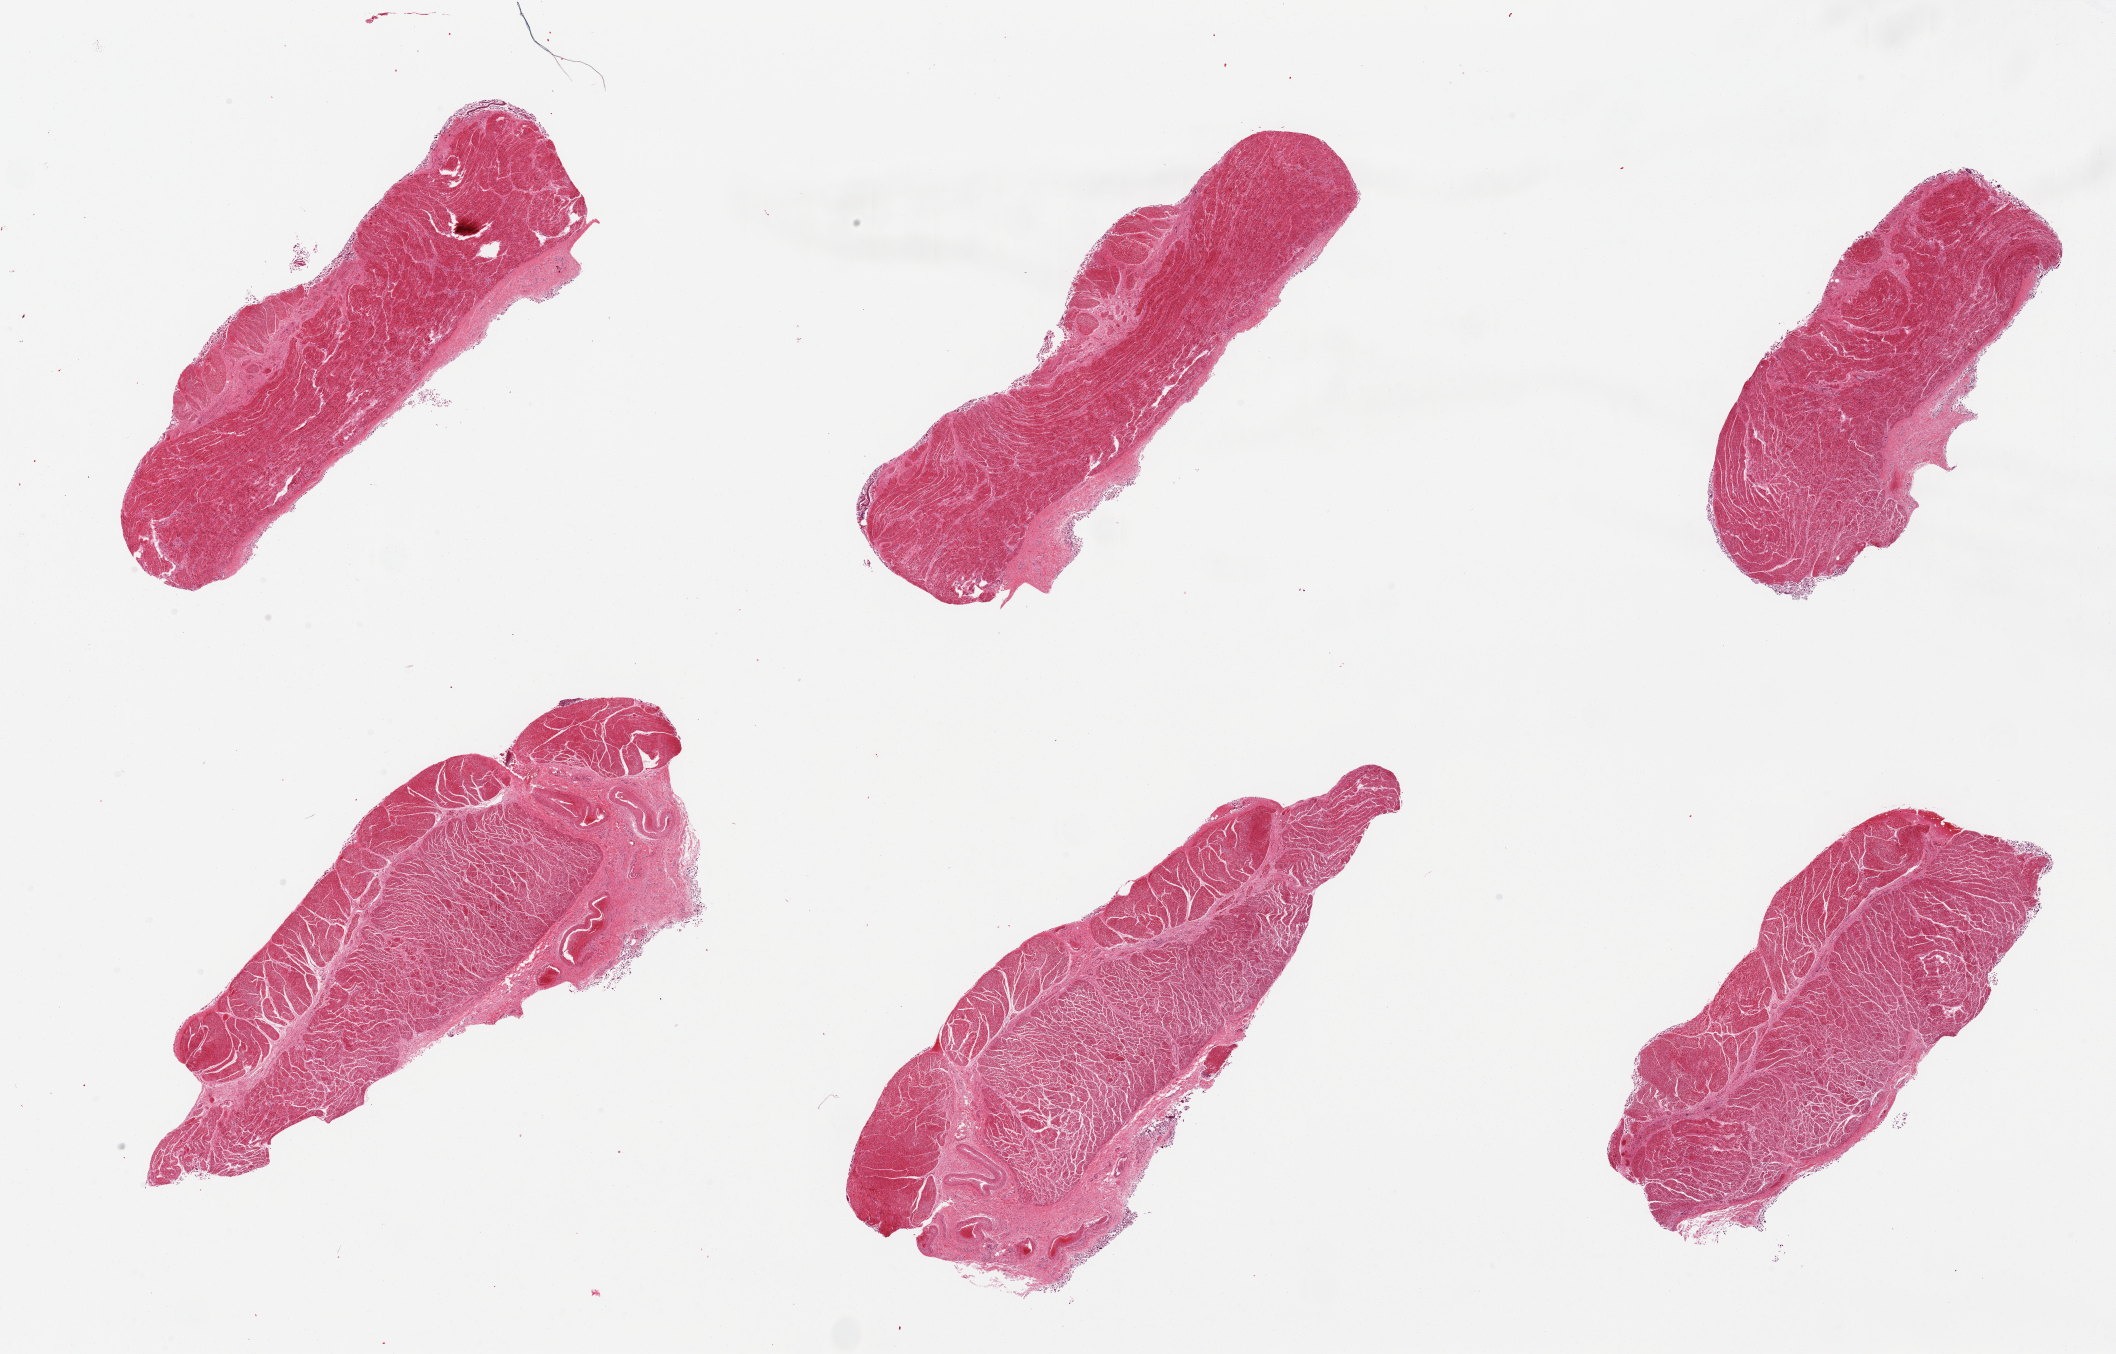
Digitized haematoxylin and eosin-stained section, brightfield, low-resolution overview of the scanned area, about 33.5 x 21.4 mm (from a 20x scan), PAXgene-fixed, paraffin-embedded tissue, sampled site (target tissue): esophageal muscle, tissue donor sample. Donor: male.
- pathologist's review note for this sample: 6 pieces, trimmed, but with abundant detached squamous (and few glandular) cells